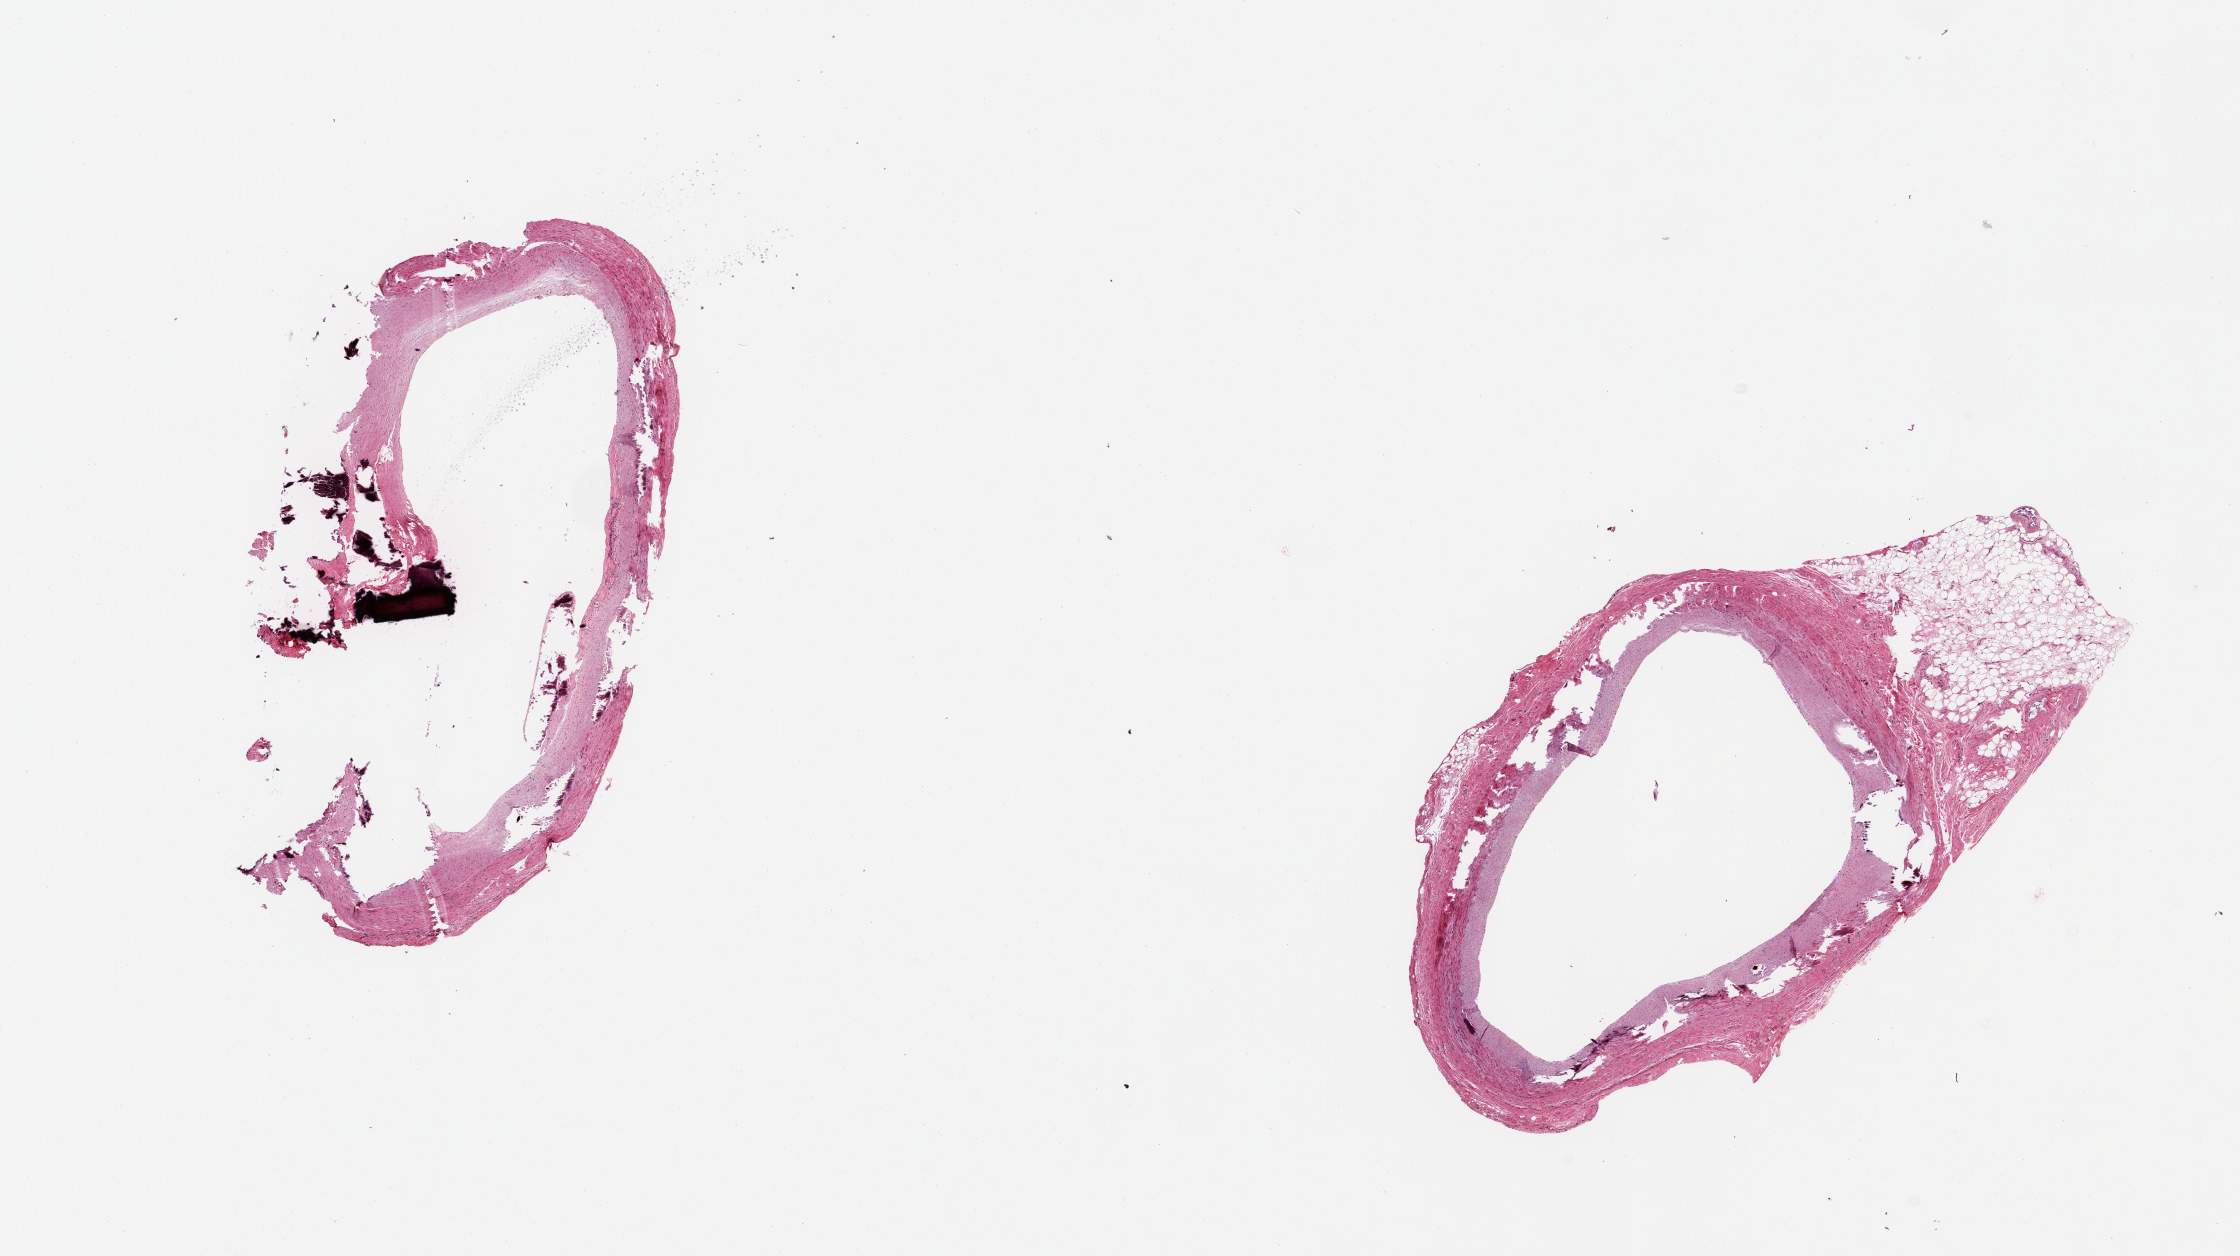
Whole-slide image, hematoxylin and eosin (H&E) stain, brightfield — low-resolution overview of the scanned area, about 17.7 x 9.9 mm (from a 20x scan). PAXgene-fixed paraffin-embedded (PFPE) section. Target tissue: coronary artery. Tissue donor sample. Donor sex: female.
* review note (as recorded): 2 pieces, ~20% occlusive calcifying atherosis